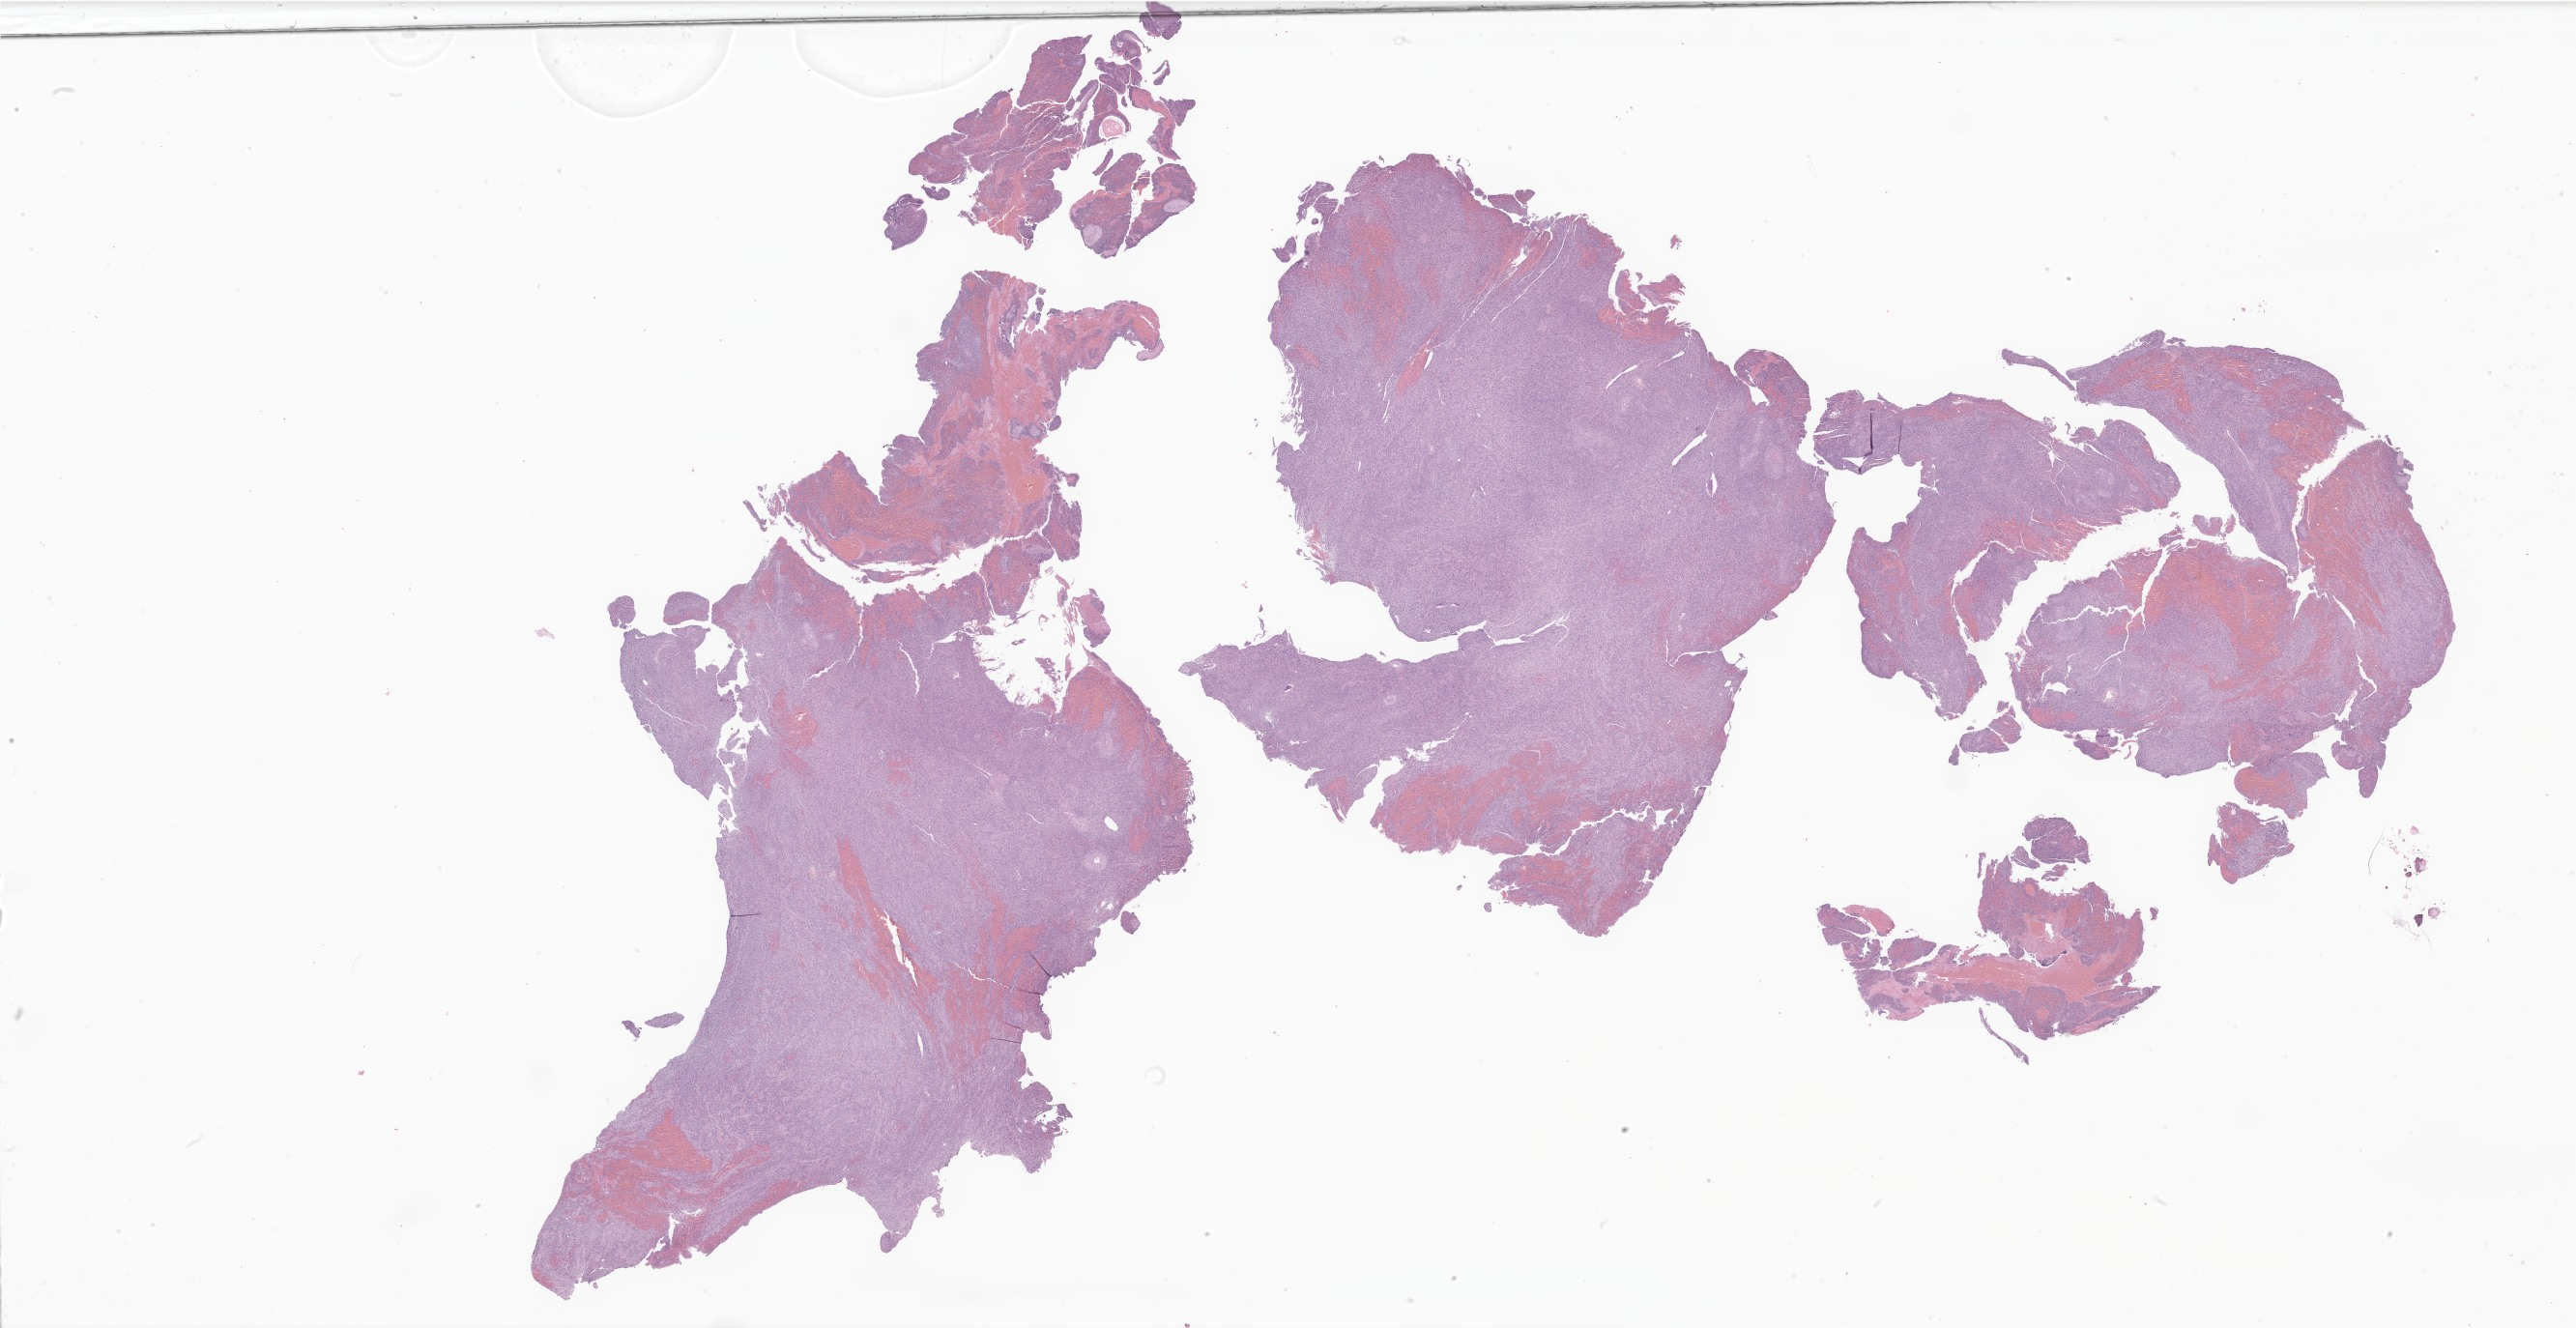
Haematoxylin and eosin whole-slide image of tumor tissue from the mandible, a low-resolution overview of the entire scanned area, about 45.0 x 23.2 mm; formalin-fixed paraffin-embedded section. Male patient, age 229 months (19 years 1 month).
• recorded diagnosis: Malignant tumor, spindle cell type